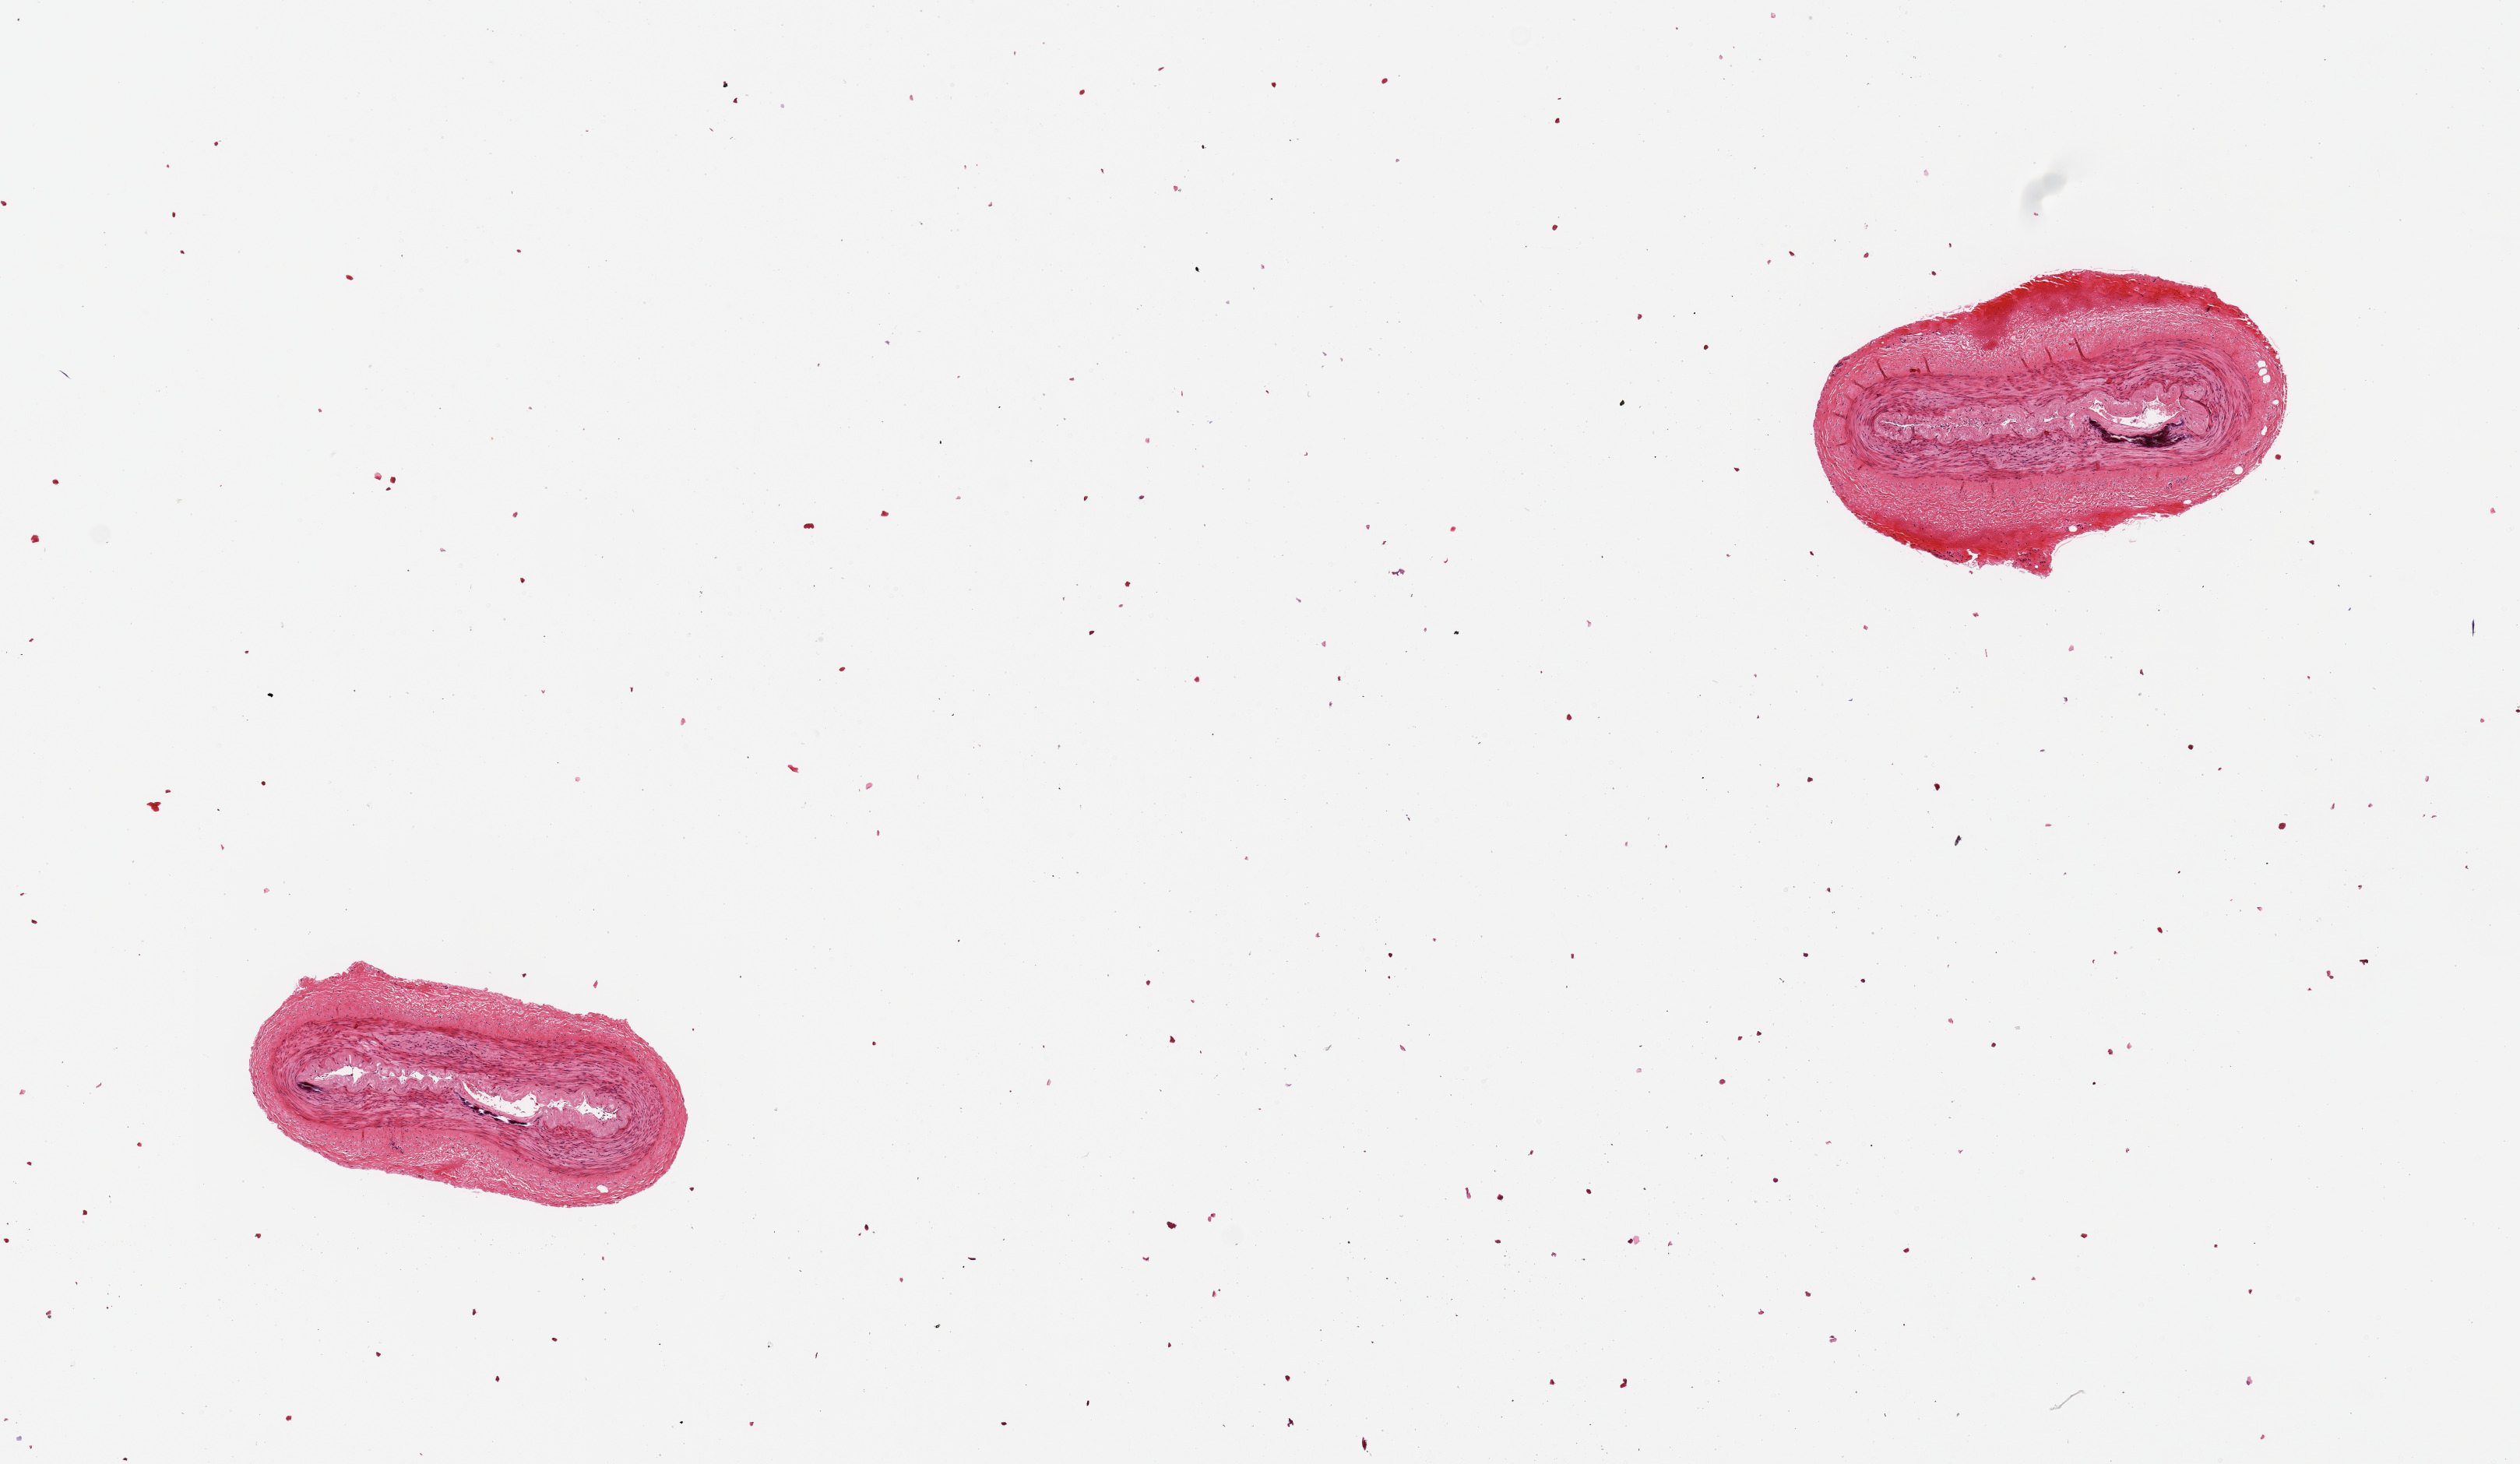
Whole-slide image, H&E stain, low-resolution overview of the scanned area, about 12.8 x 7.4 mm (acquisition: 20x scan). PAXgene-fixed, paraffin-embedded tissue. Target tissue: tibial artery. Tissue donor sample. Donor sex: female.
* reviewer comment on this tissue sample: 2 pieces, clean specimens